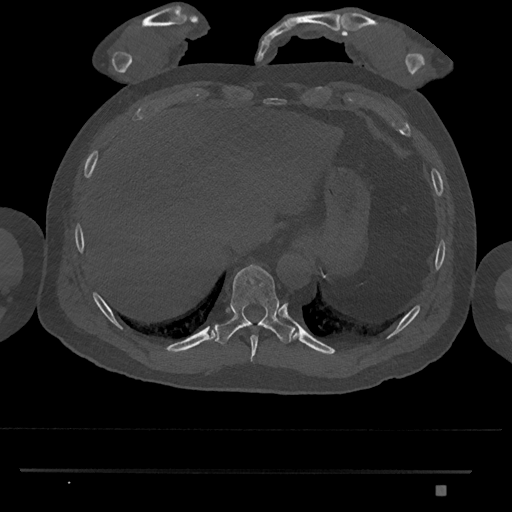
CT including the spine, one axial slice. Slice 1014 of 1134 in the series (ordered by position). Reconstruction kernel Br40s/3. 120 kVp. Bone window (W 1800 / L 400 HU). 512 × 512 image matrix, field of view 429 × 429 mm. Male patient, age 65 years. From the clinical record (not read from this slice): primary cancer: prostate.
Outlined on this slice (semi-automatic segmentation, software-assisted and operator-edited):
- T10 vertebra: bounding box <214,264,293,345> (left, top, right, bottom; pixels)
- T9 vertebra: <250,335,259,362>